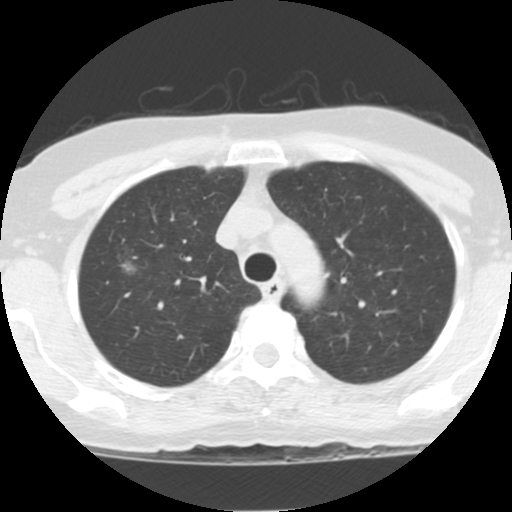
Low-dose screening chest CT, axial slice, second annual screen, lung window (W 1500 / L -600 HU), 2.5 mm slice thickness, standard (soft-tissue) reconstruction kernel (STANDARD), 120 kVp. Female participant, aged 62 years at enrolment. Current smoker at enrolment.
- Lesion marked by an expert reader, bounding box [x1, y1, x2, y2] px = [107, 248, 151, 292].
- Screening reader's record for this exam (one nodule recorded; not confirmed to be the boxed lesion): non-calcified nodule or mass ≥4 mm, right upper lobe, 8 × 7 mm, poorly defined margins, ground glass attenuation, pre-existing on the prior screen: yes; interval growth: yes.